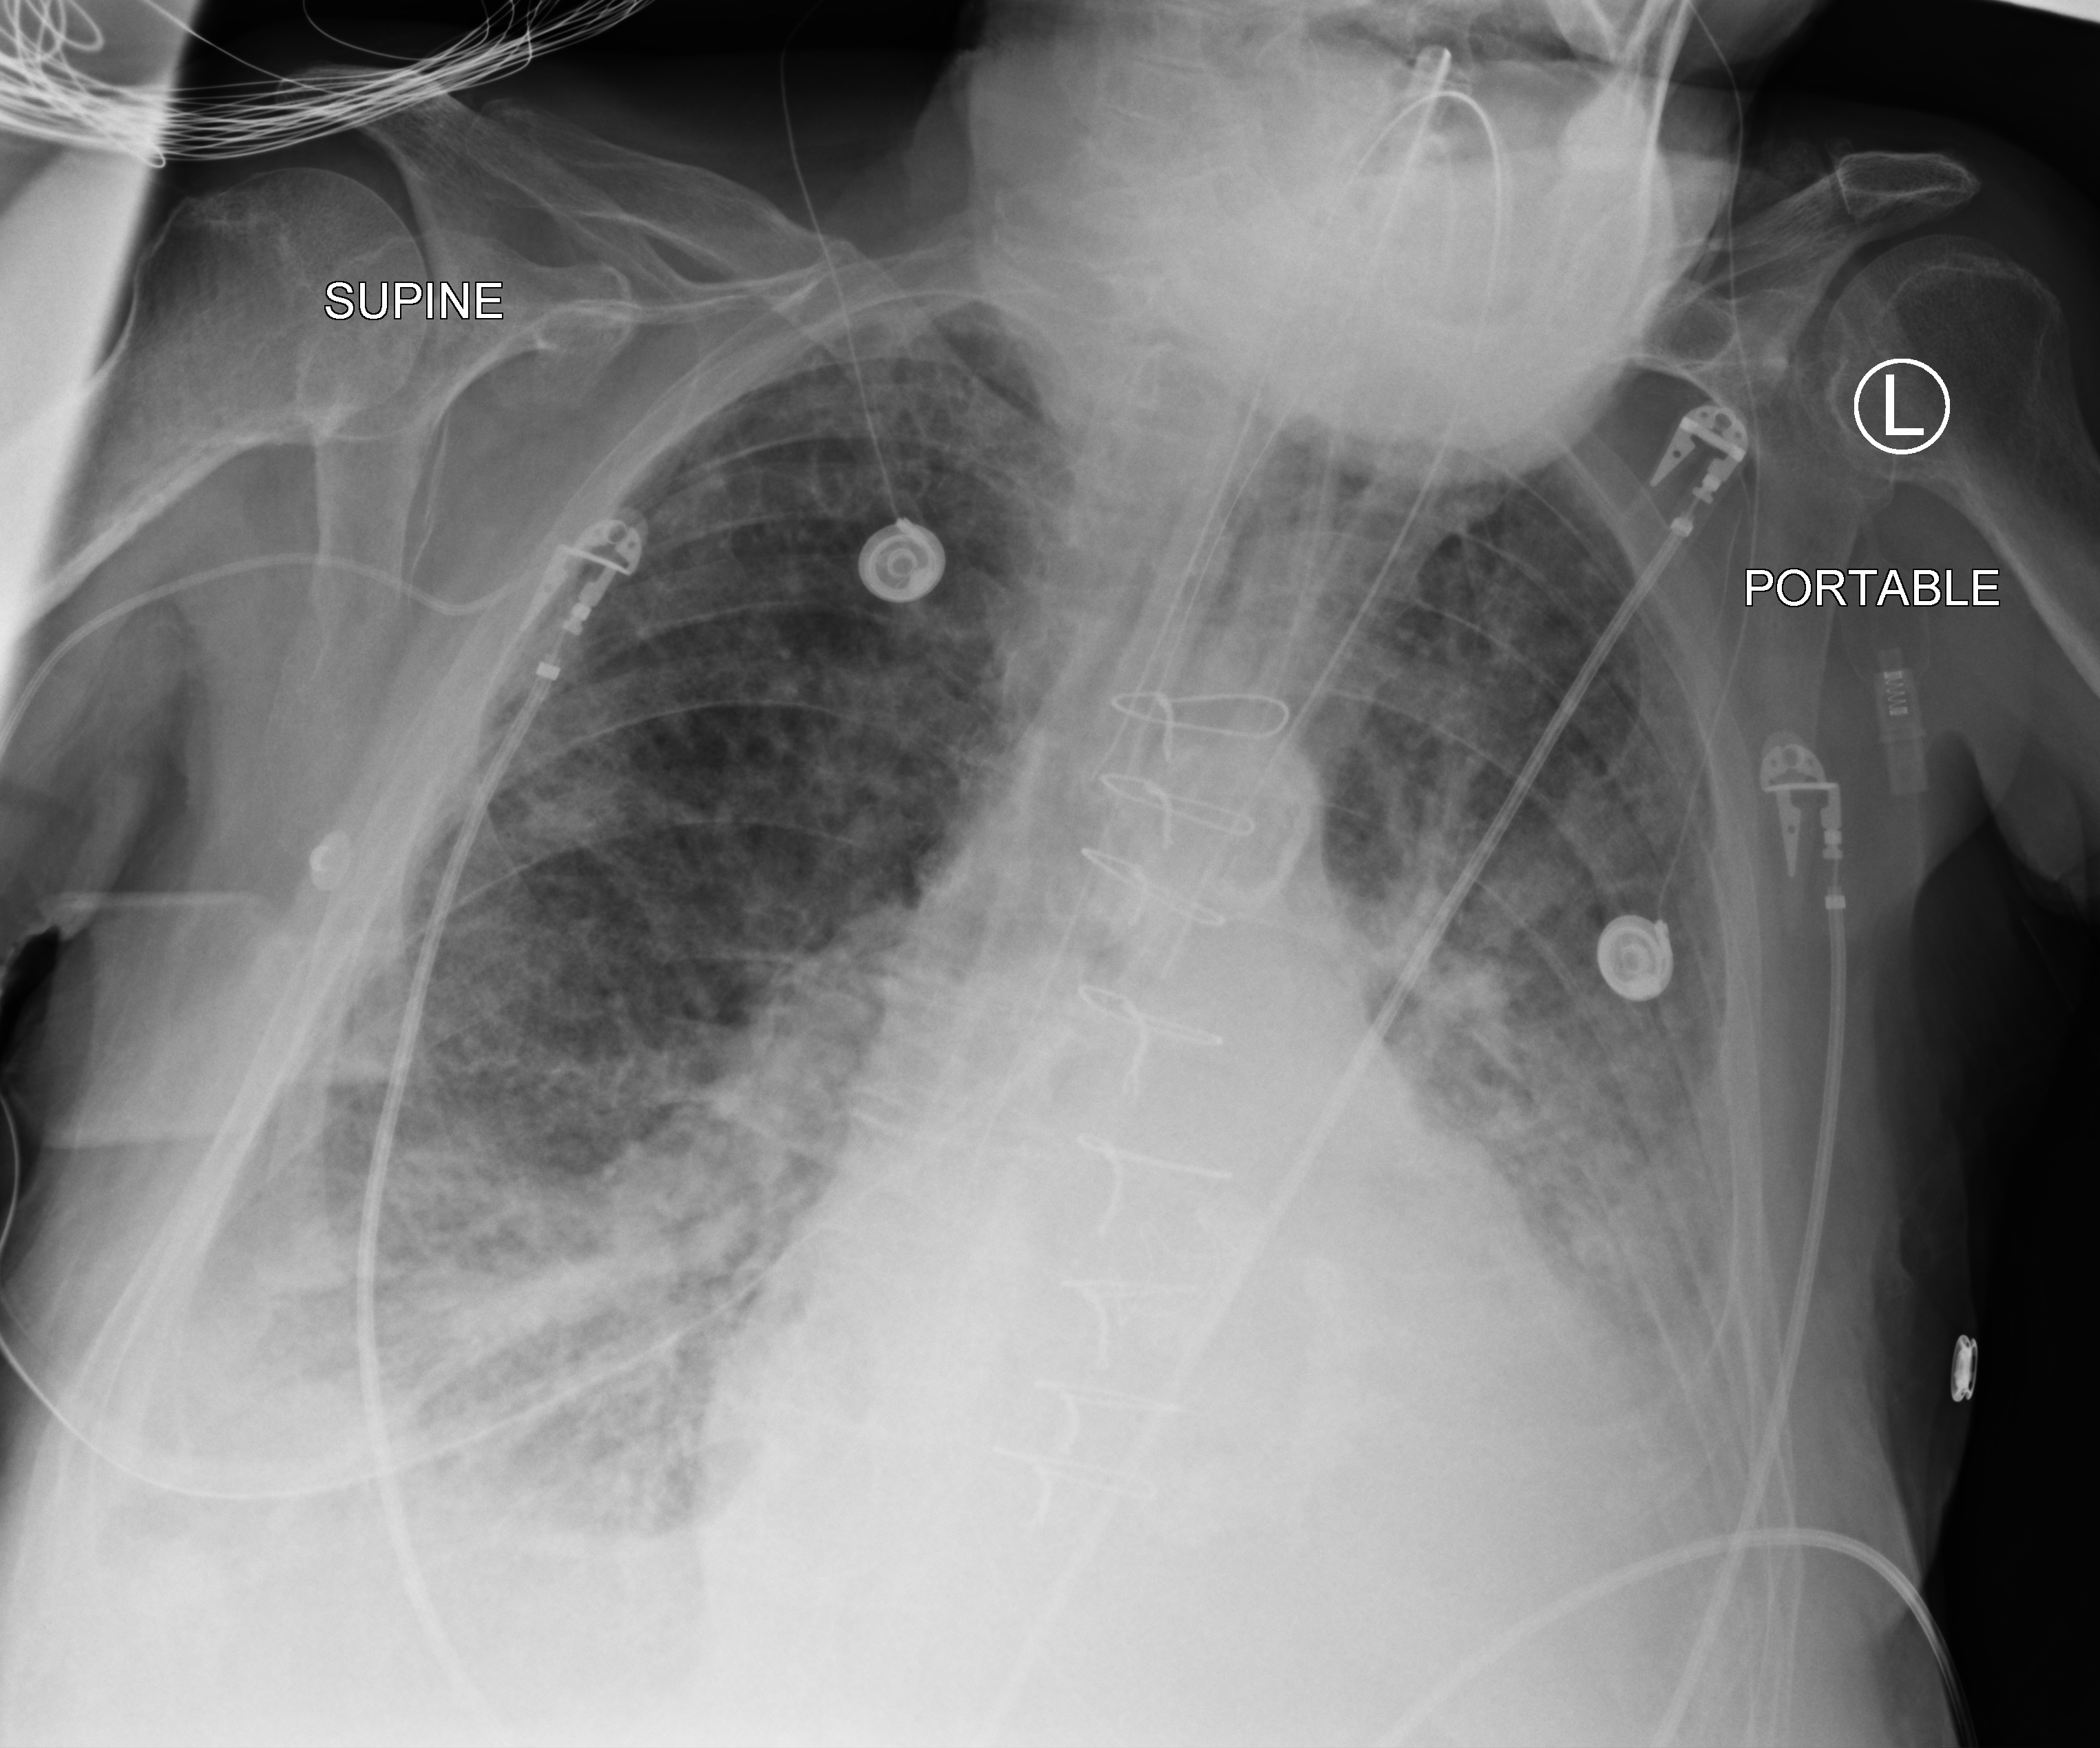
Portable chest radiograph. Patient hospitalised with COVID-19; male, aged 75–90 years.
Admission-level facts for this patient (not findings on this image; timing relative to this image not recorded):
- length of hospital stay: 40 days